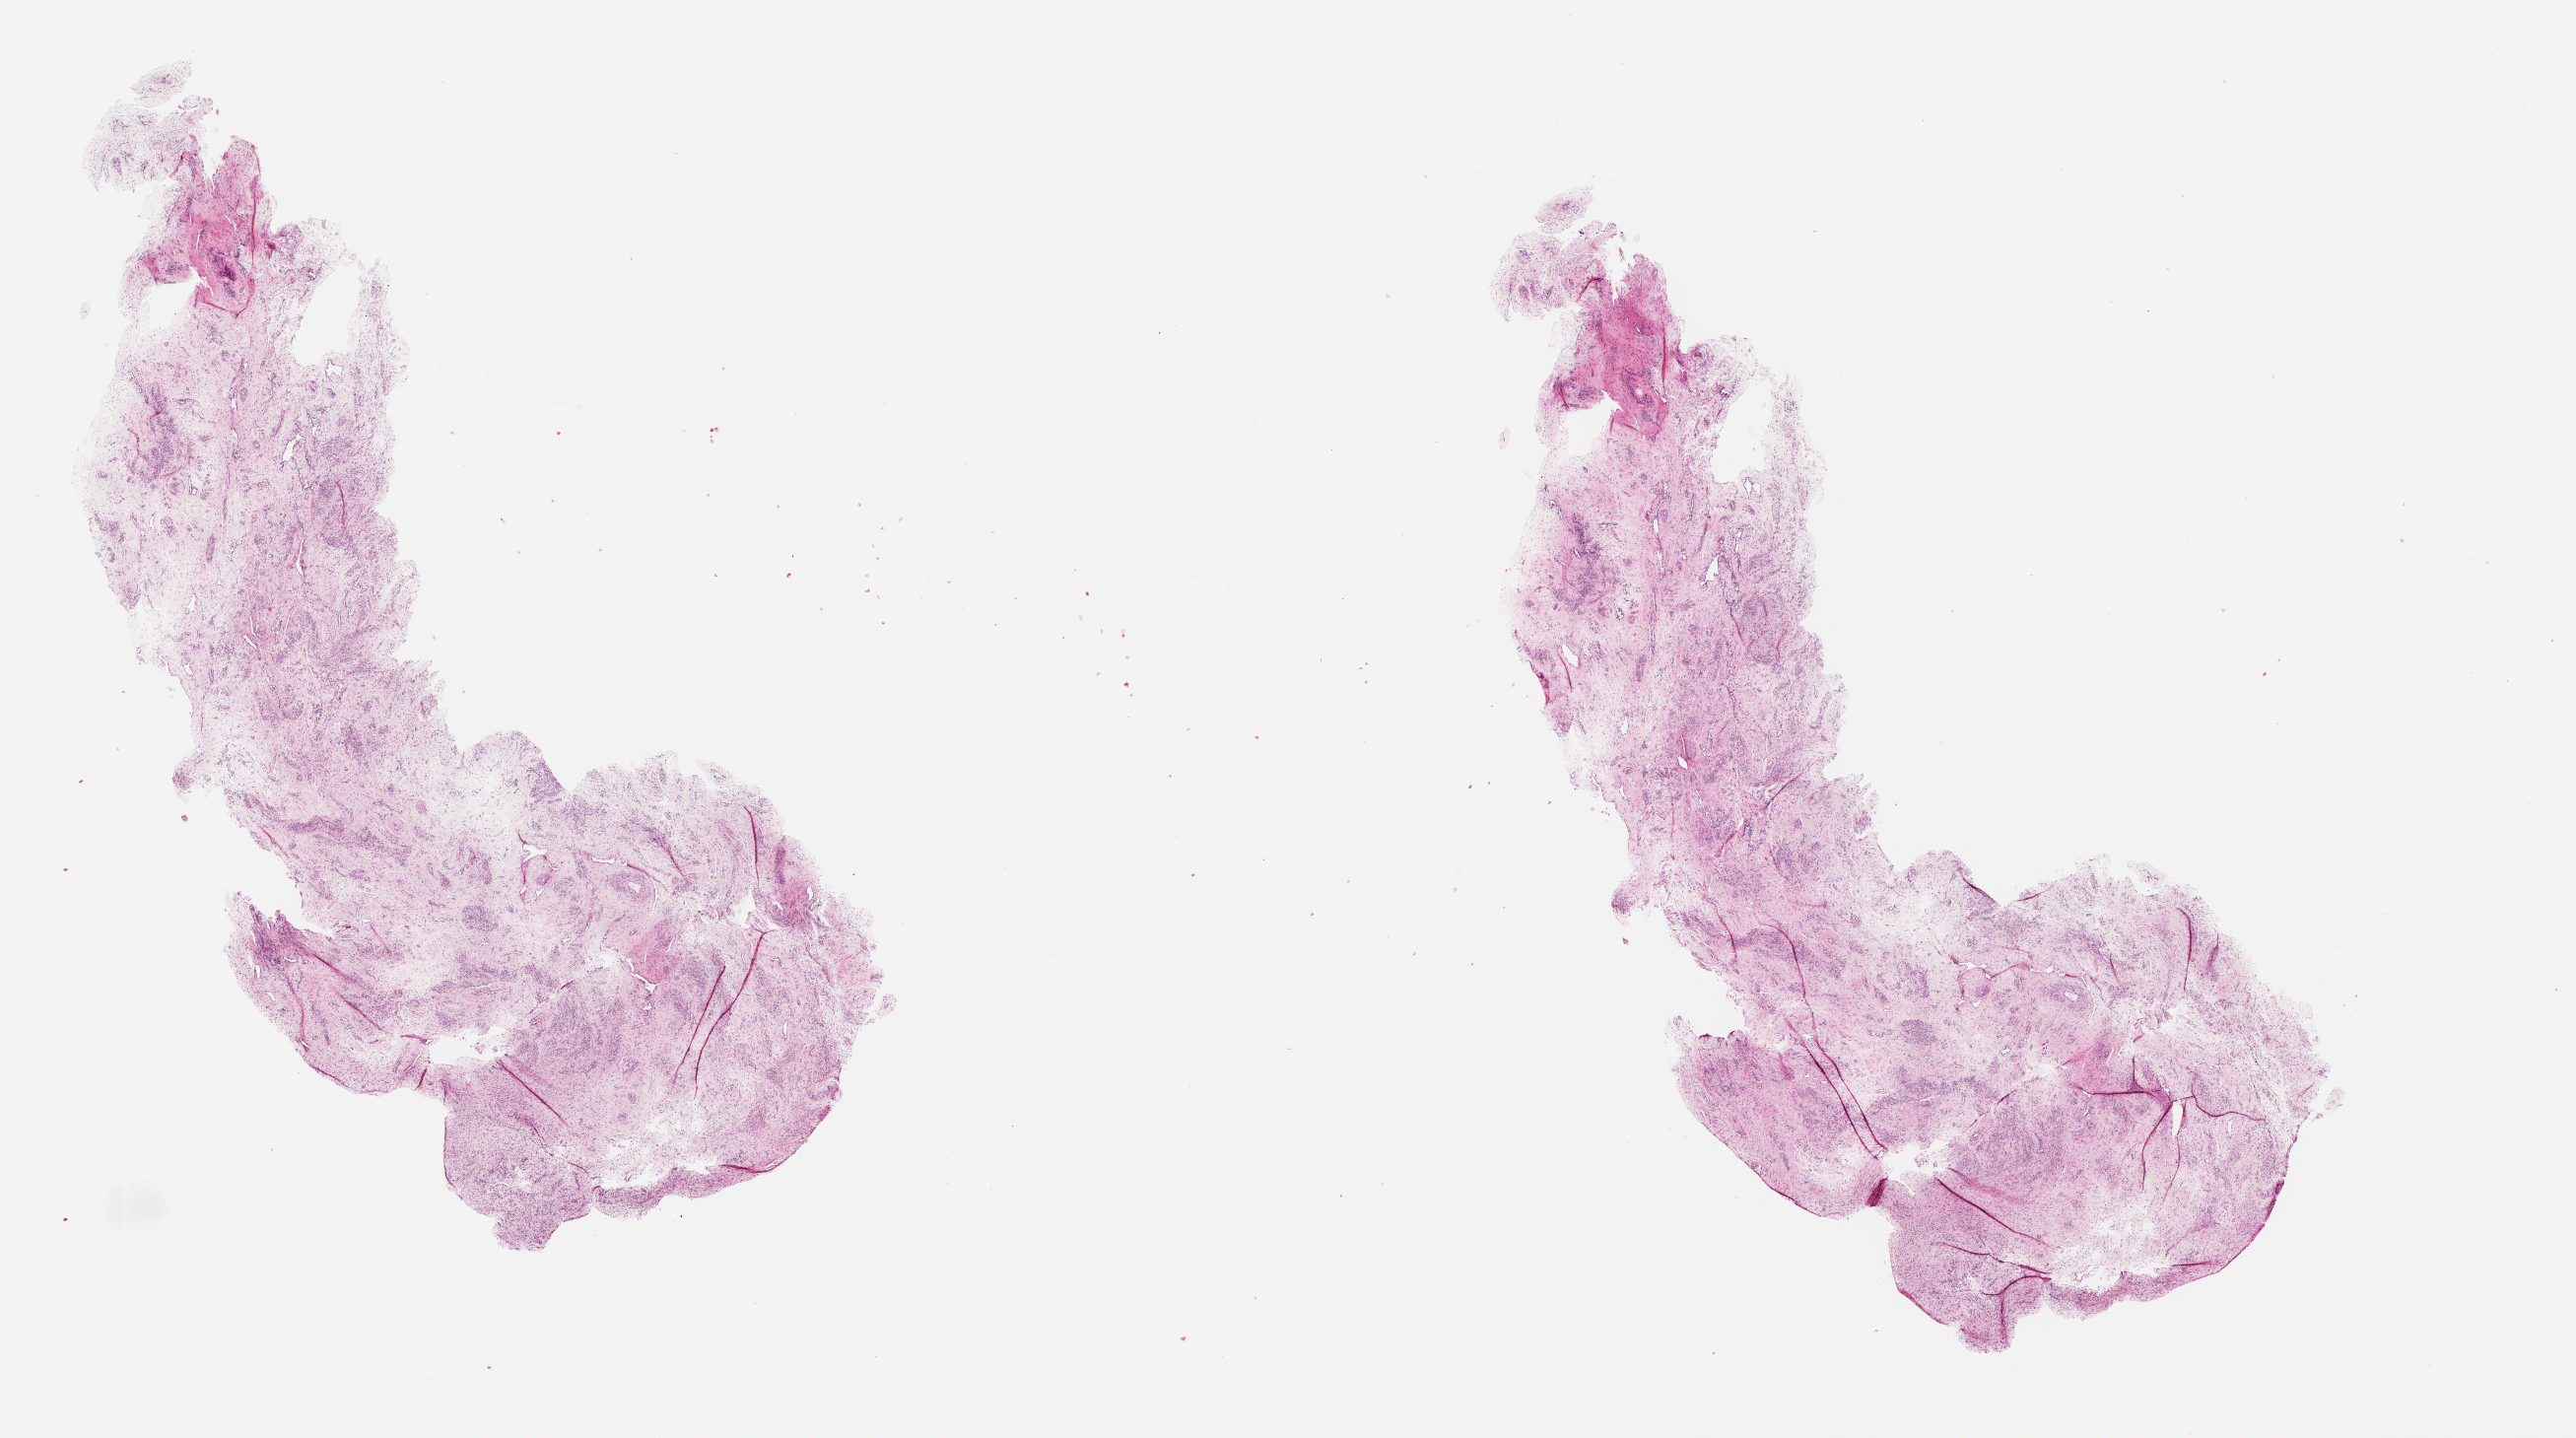
Hematoxylin and eosin (H&E) stained whole-slide image — a low-resolution overview of the entire scanned area, about 21.0 x 11.7 mm (slide scanned at 20x), uterus, tissue type not recorded.
* patient diagnosis (cohort enrolment): corpus endometrial carcinoma (uterus)